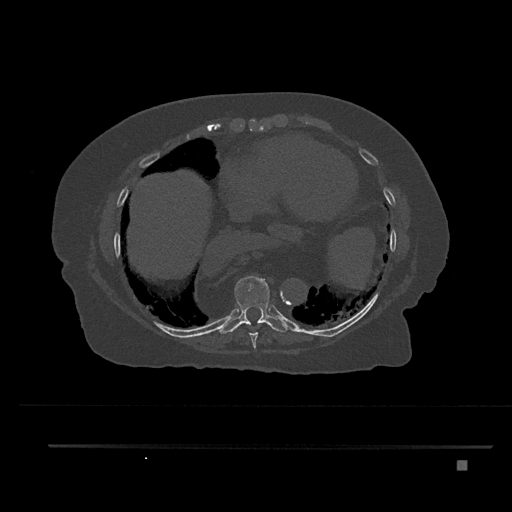
CT including the spine, one axial slice. Position 413 of 797 along the scan axis. Reconstruction kernel Br40s/3. 120 kVp. Bone window (W 1800 / L 400 HU). 0.5 mm slice thickness. 512 × 512 image matrix. Patient: female, 76 years. From the clinical record (not read from this slice): primary cancer: lung.
Structures marked on this image (semi-automatic segmentation, software-assisted and operator-edited):
- T8 vertebra: bounding box (x1, y1, x2, y2) in pixels: (249, 332, 258, 348)
- T9 vertebra: (218, 276, 289, 334)